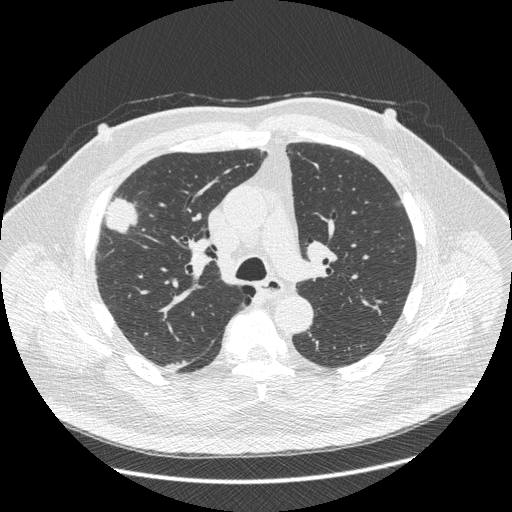
Chest CT (low-dose screening protocol), one axial image; third annual screen; lung window (W 1500 / L -600 HU); 1.25 mm slice thickness; standard (soft-tissue) reconstruction kernel (STANDARD); 512 × 512 image matrix. Male, age 66 years at enrolment.
• Lesion marked by an expert reader, box from (x=86, y=183) to (x=145, y=265) px.
• Screening reader's record for this exam (one nodule recorded; not confirmed to be the boxed lesion): non-calcified nodule or mass ≥4 mm, right upper lobe, 48 × 25 mm, spiculated (stellate) margins, soft tissue attenuation, pre-existing on the prior screen: no.
• Participant outcome: lung cancer diagnosed 35 days after this screen — non-small cell carcinoma, right upper lobe, stage IV (AJCC 6th edition), 50 mm at pathology.